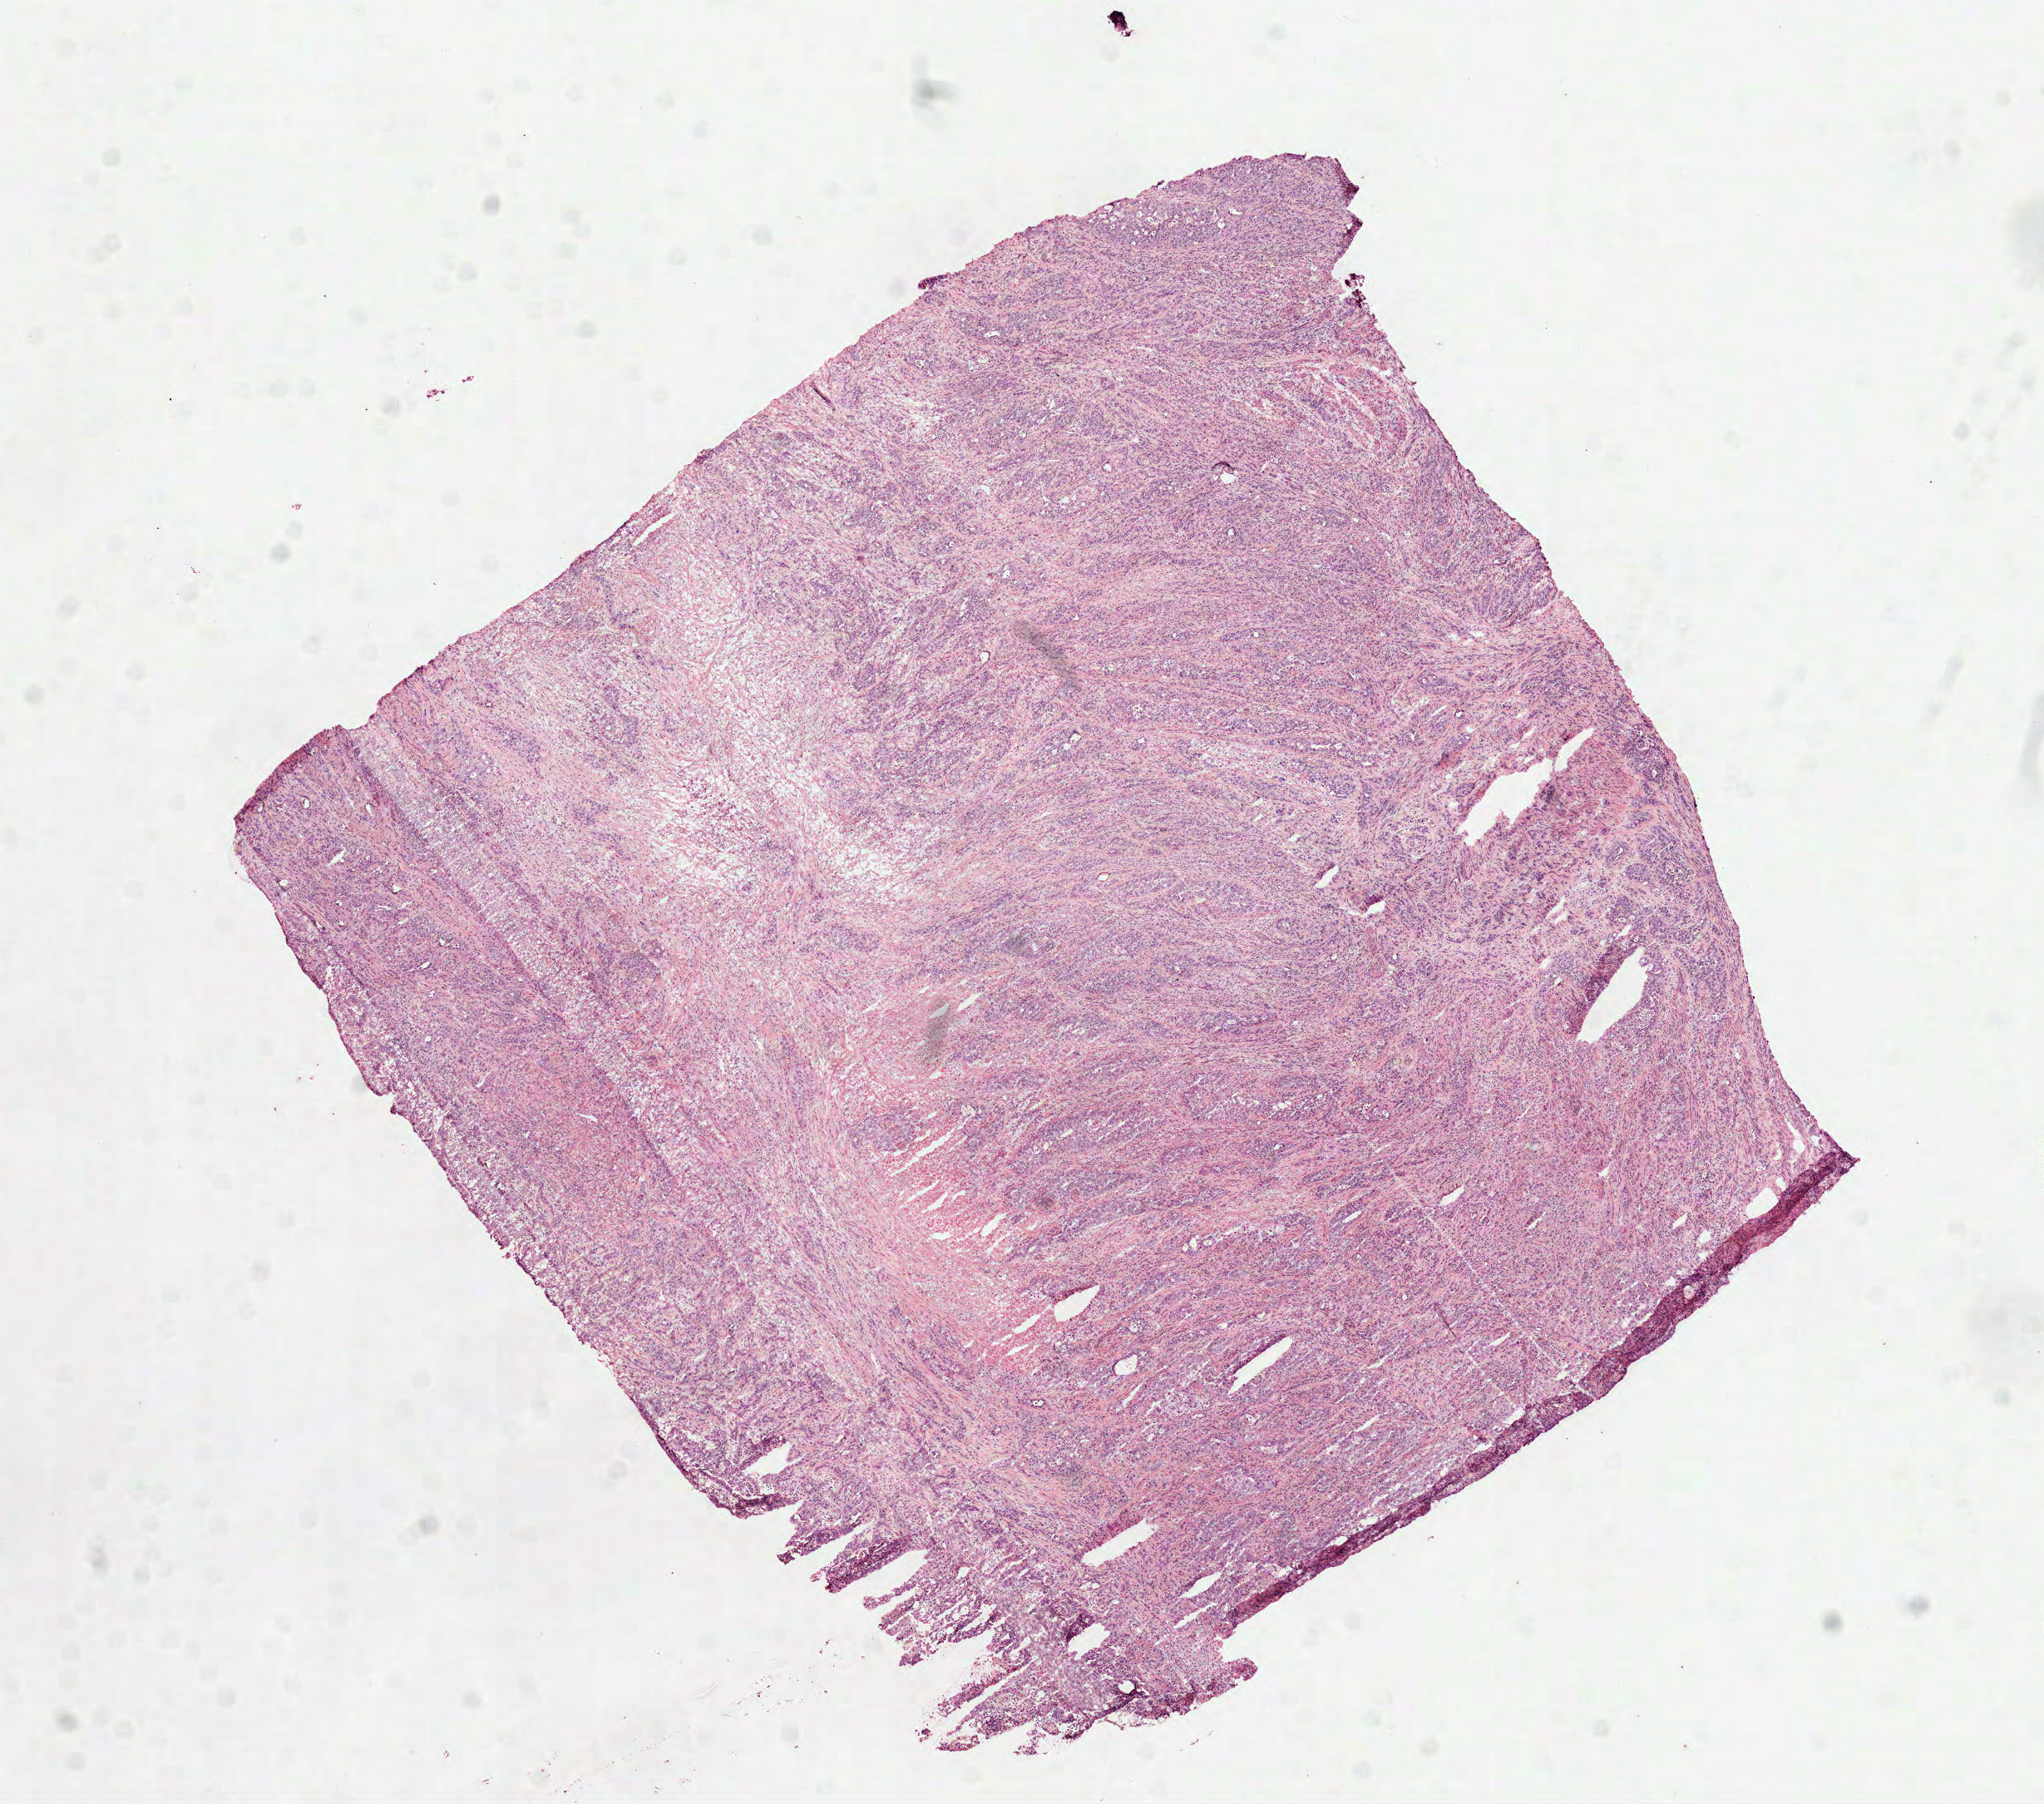
H&E-stained whole-slide image, whole scanned area (about 9.9 x 8.7 mm, from a 40x scan) shown as a low-resolution overview. Frozen section from the top of the tissue portion. Primary tumour sample from the stomach. Male, age 58 years at initial diagnosis. Histologic grade: G3 (poorly differentiated). Pathologist review of this section (percent, as recorded): tumour cells 77%, tumour nuclei 80%, normal cells 0%, stromal cells 20%, necrosis 3%.
Histologic diagnosis: Carcinoma, diffuse type (cardia, NOS). Lymph nodes positive (case pathology): 6 of 9 examined. AJCC pathologic stage: IIIA (6th edition).